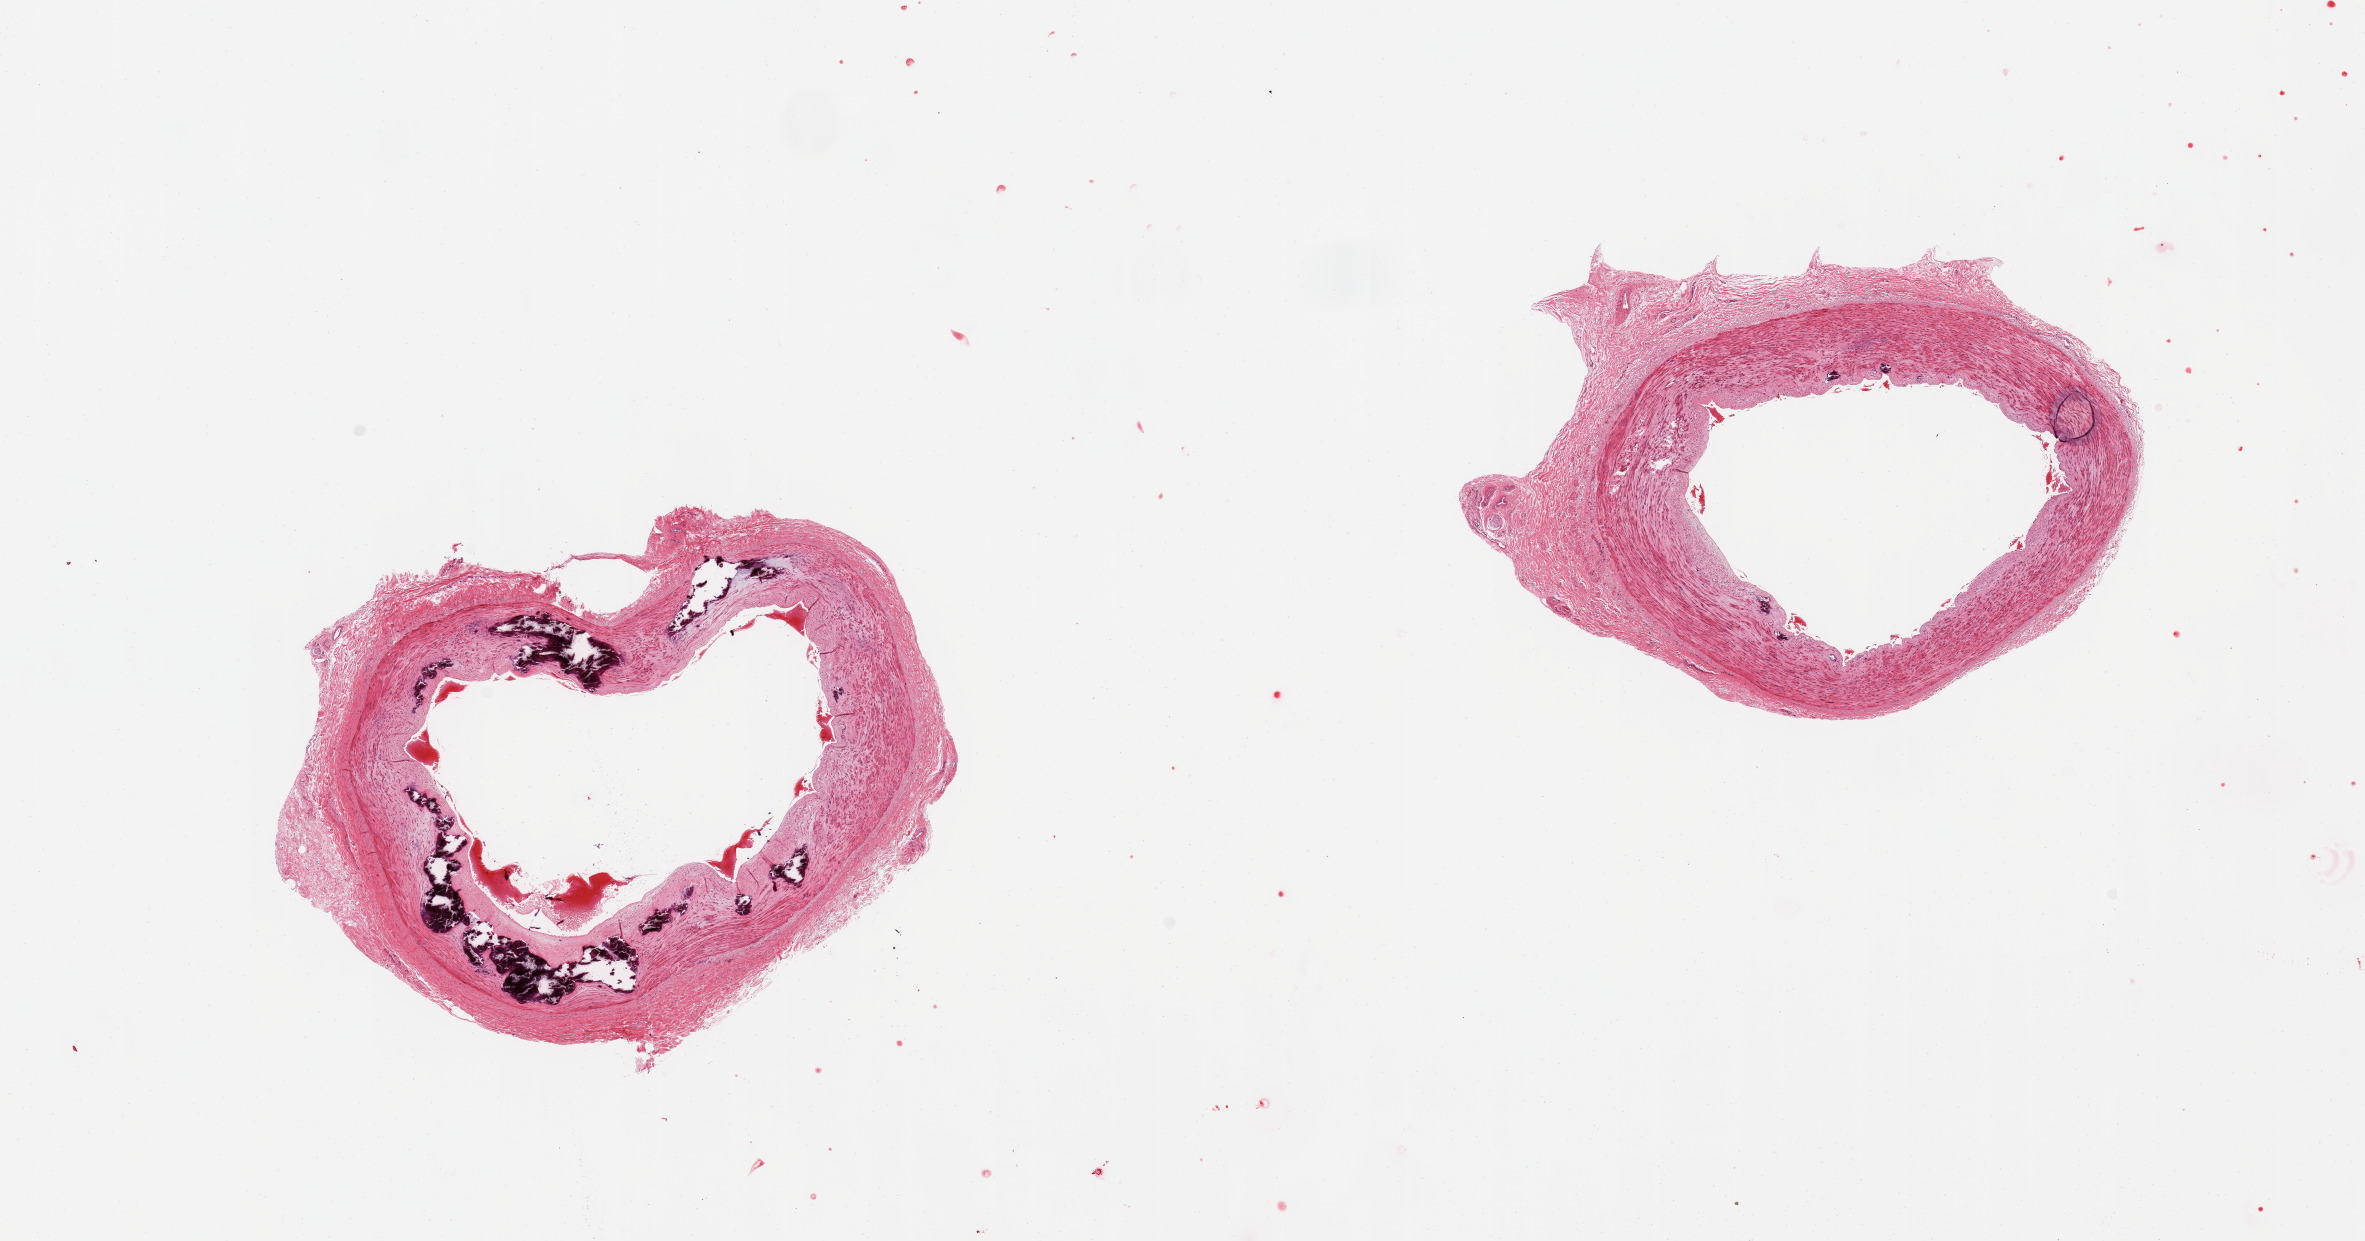
Digitized haematoxylin and eosin-stained section, shown as a low-resolution overview of the whole scanned area (about 18.7 x 9.8 mm, acquisition: 20x scan), PAXgene-fixed paraffin-embedded (PFPE) section, section of tibial artery (target tissue), tissue donor sample. Donor sex: male.
- reviewer comment on this tissue sample: 2 pieces, minimal atherosis; prominent Monckeberg sclerosis; Rim of adherent fibrous tissue up to ~1mm